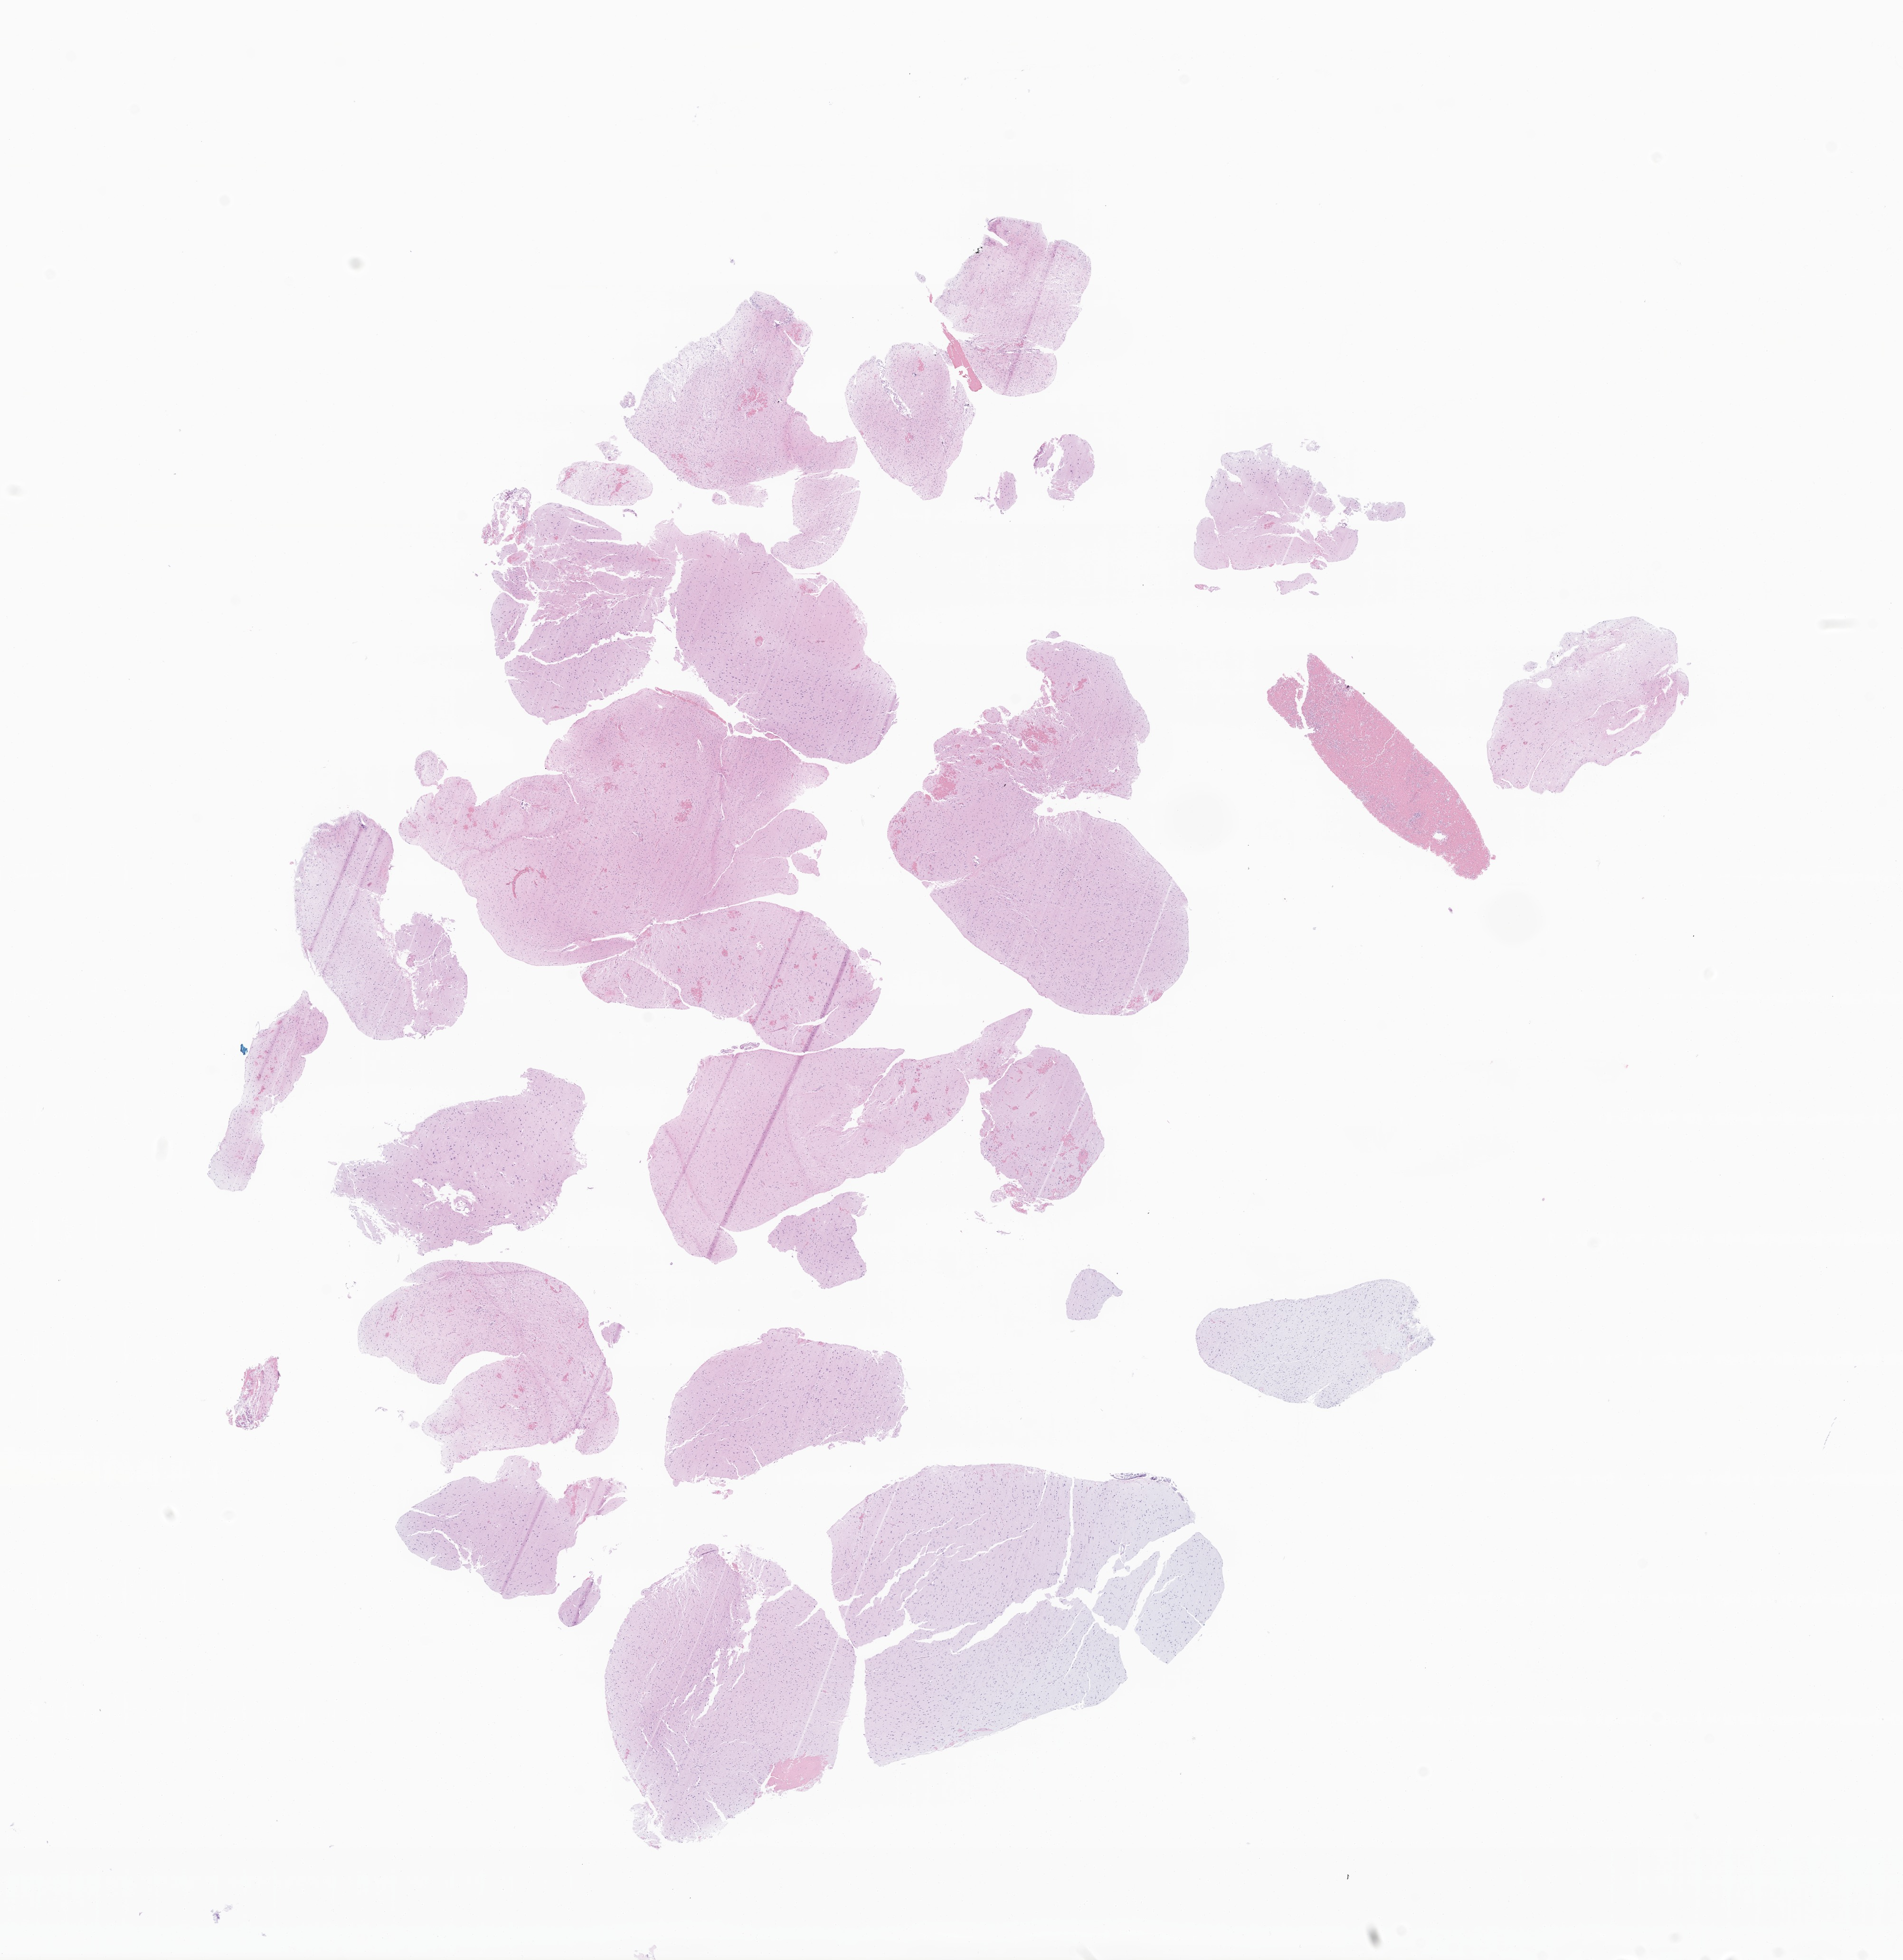
Digitized H&E-stained section of tumor tissue from the brain — a low-resolution overview of the entire scanned area, about 16.9 x 17.4 mm, formalin-fixed, paraffin-embedded (FFPE) tissue. Patient female; age 62 months (5 years 2 months).
Diagnosis: Glioma, malignant.